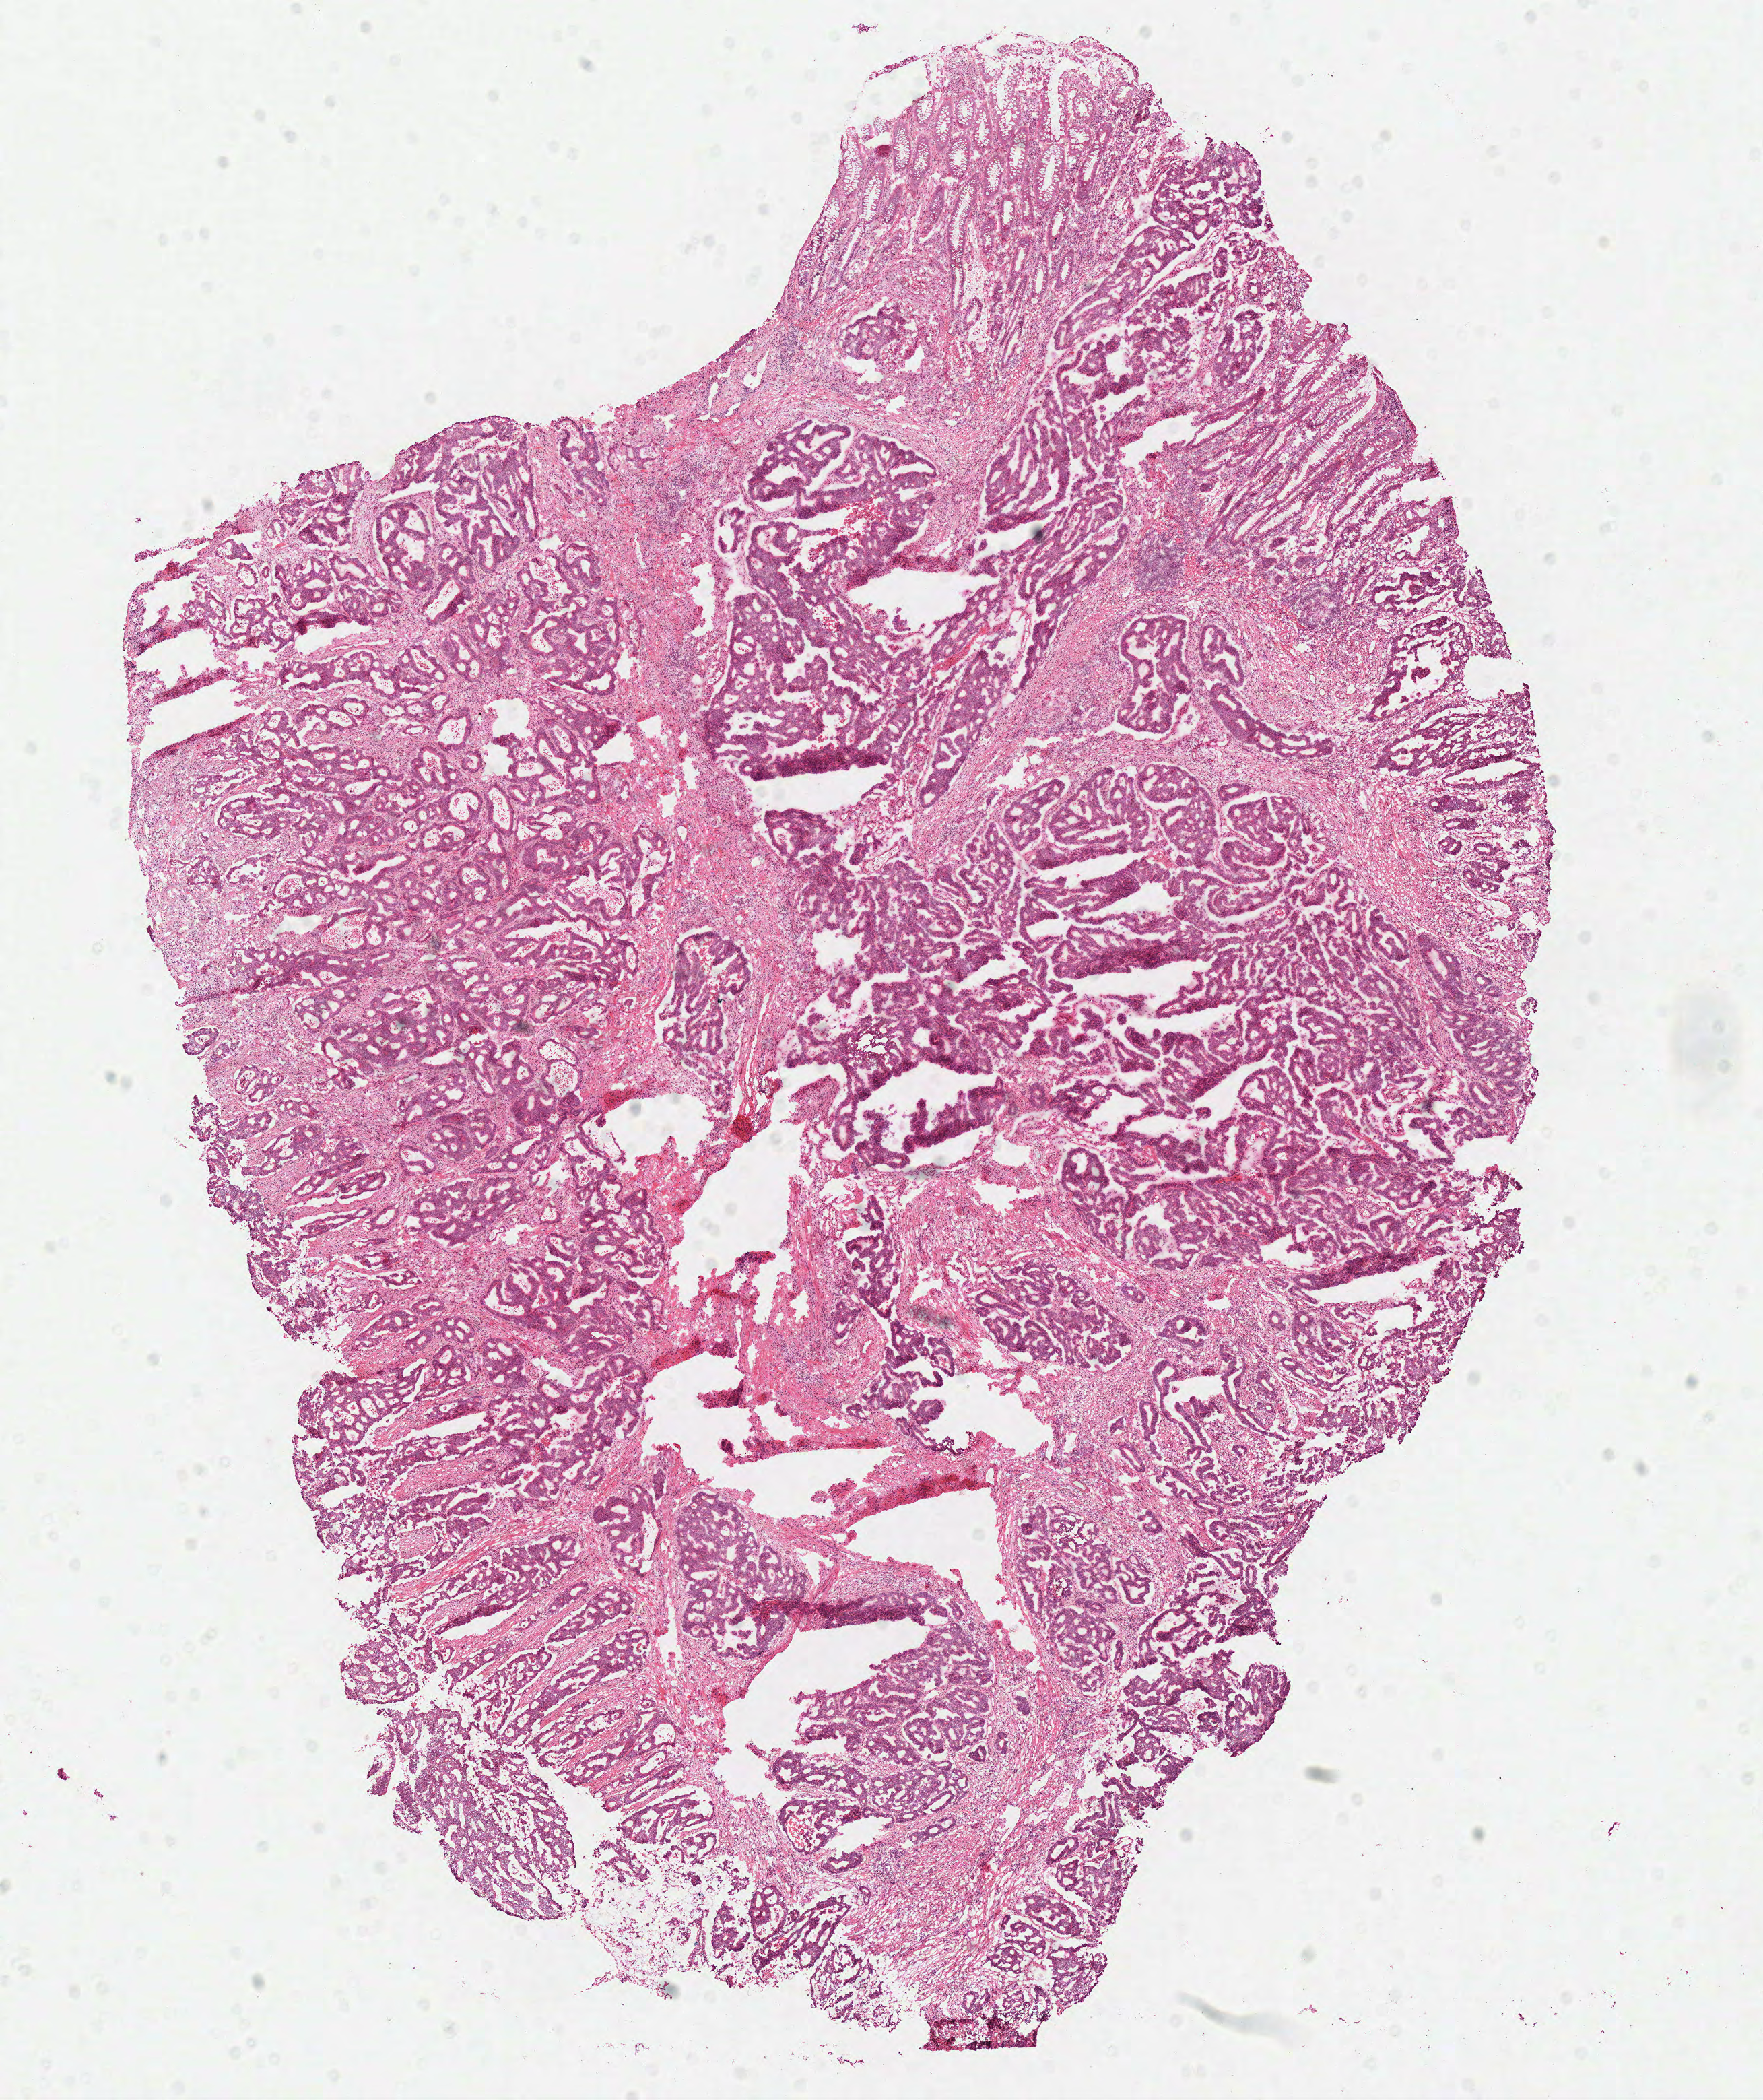
Digitized Hematoxylin and eosin (H&E) stained tissue section (whole slide), whole scanned area (about 10.3 x 12.3 mm, slide scanned at 40x) shown as a low-resolution overview; frozen section; sample: primary tumour, rectum. Patient: male, age at initial diagnosis 48 years. Pathologist review of this section (percent, as recorded): tumour cells 80%, tumour nuclei 80%, normal cells 0%, stromal cells 15%, necrosis 5%.
* lymph nodes positive (case pathology): 0 of 21 examined
* AJCC pathologic stage: I (6th edition)
* histologic diagnosis: Adenocarcinoma, NOS (rectosigmoid junction)